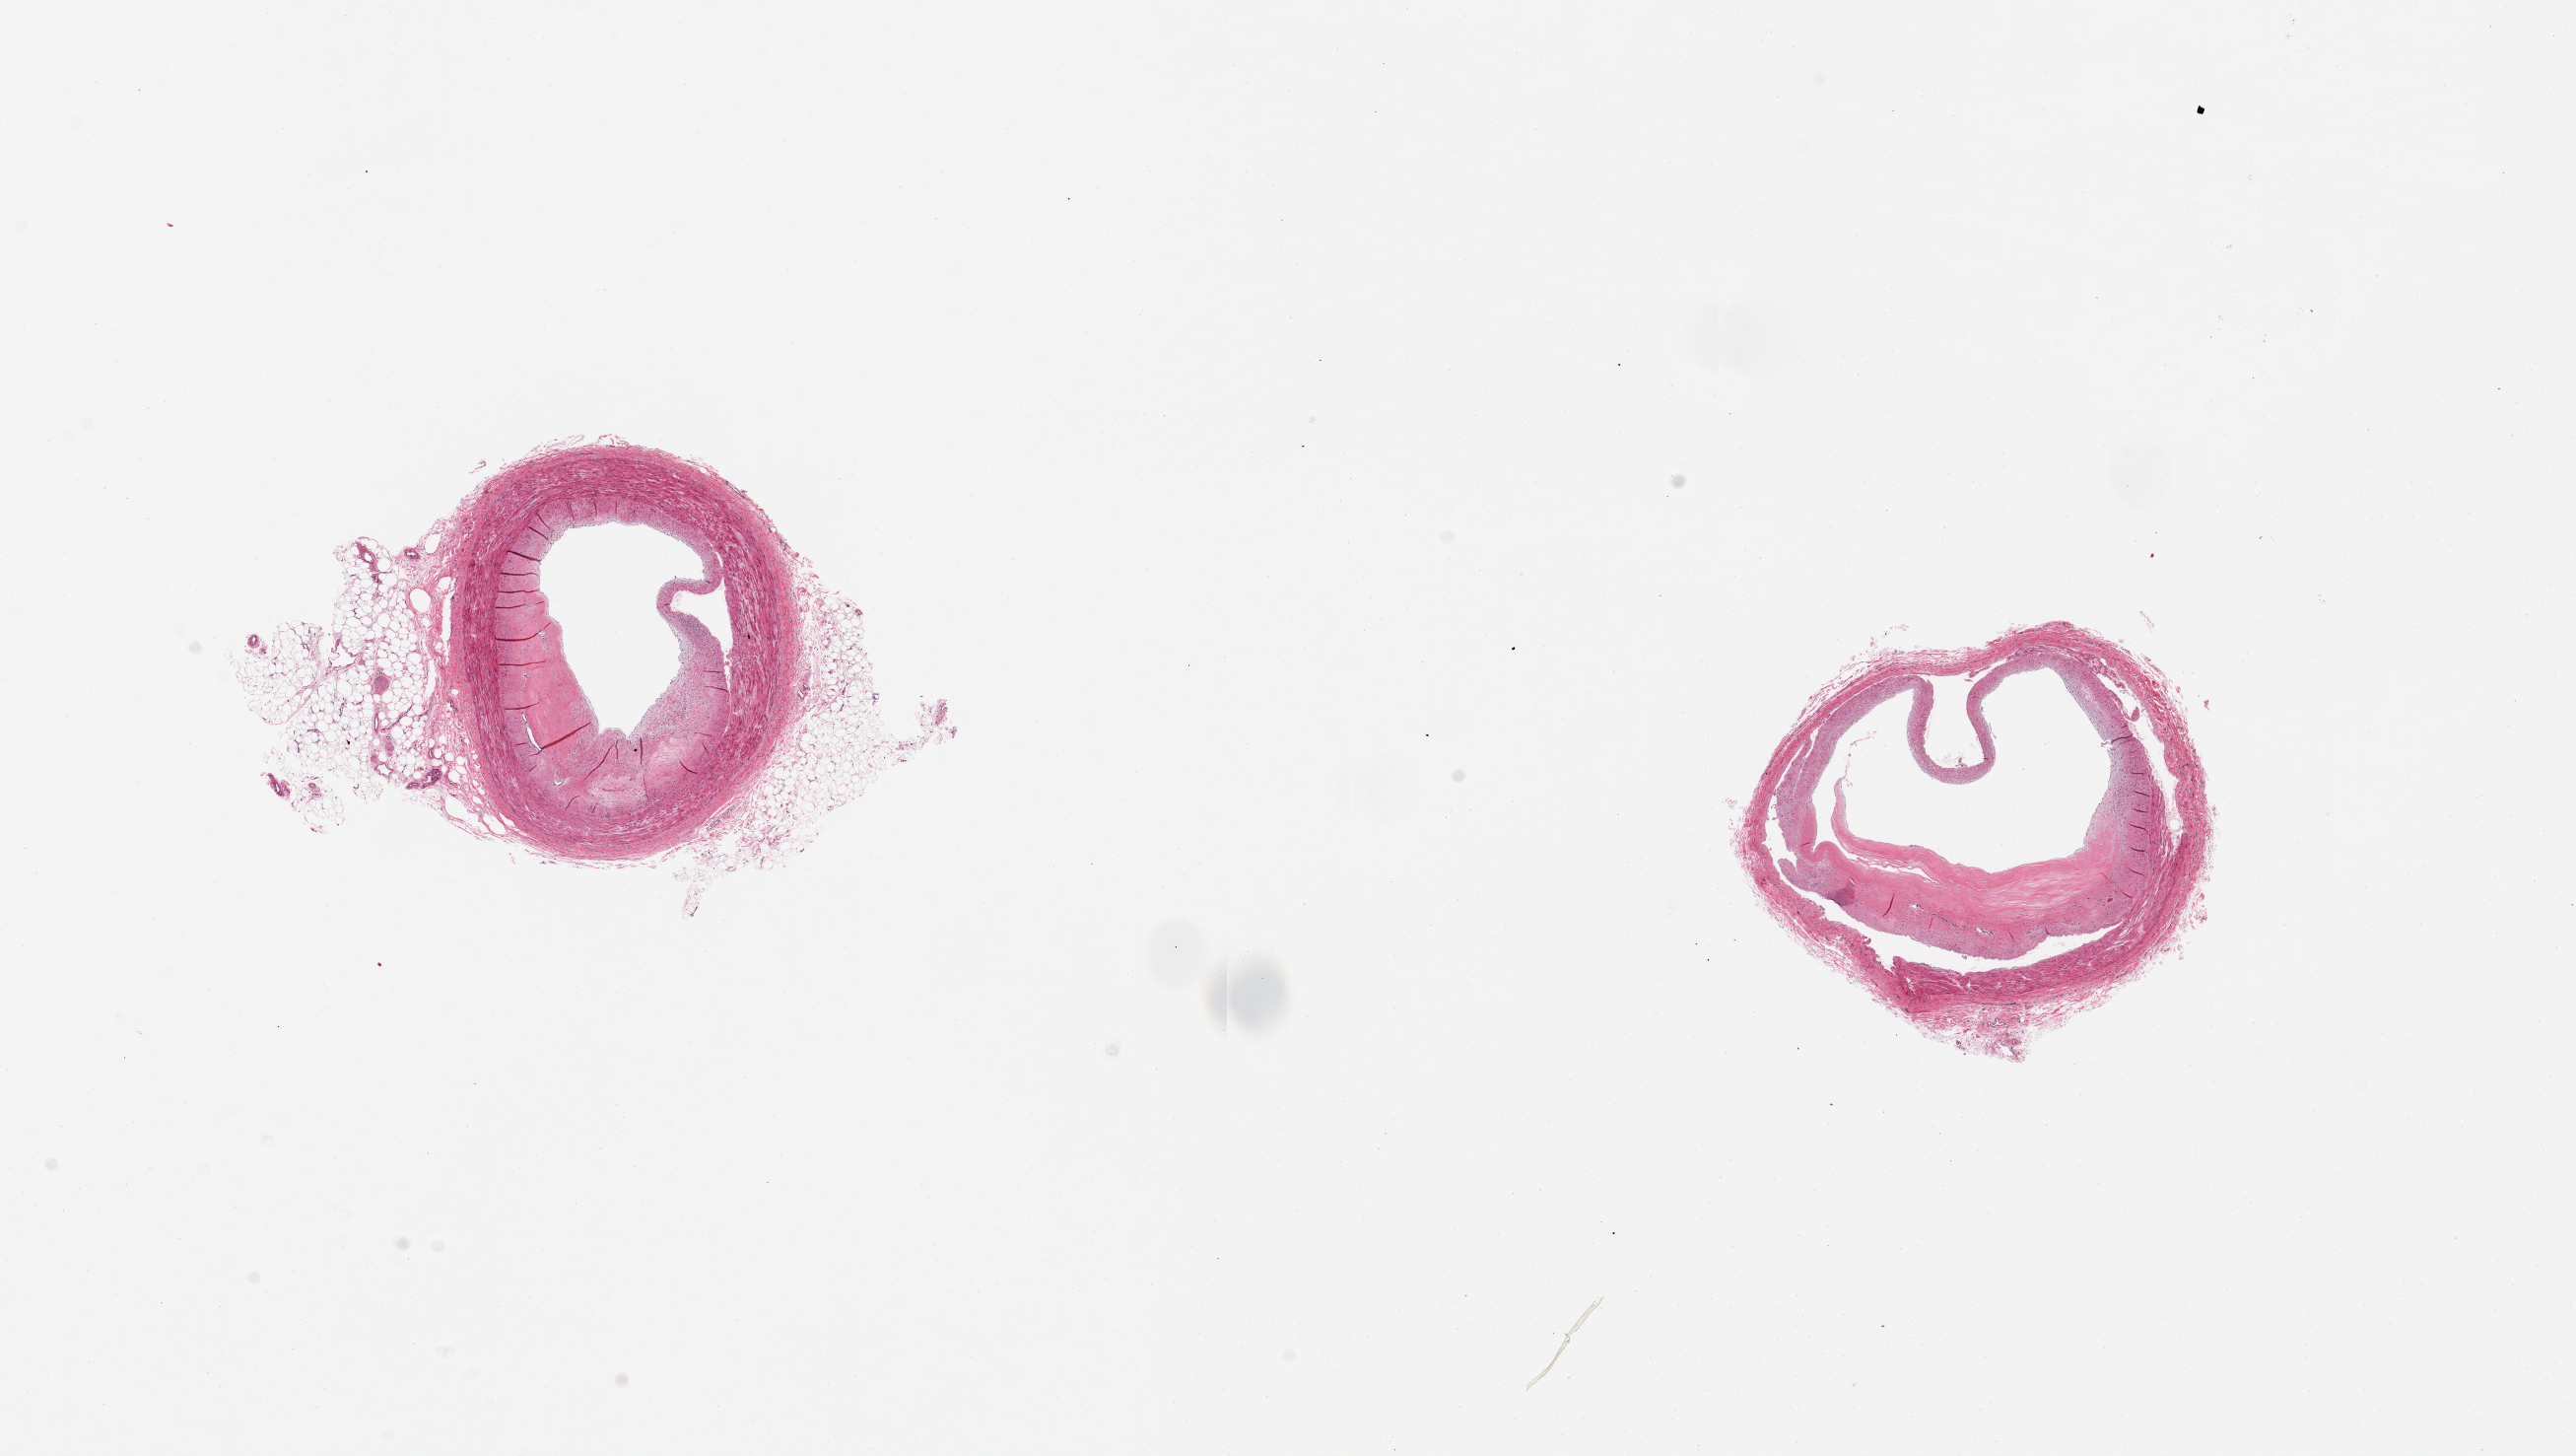
Haematoxylin and eosin whole-slide image, brightfield, shown as a low-resolution overview of the whole scanned area (about 20.7 x 11.7 mm). PAXgene-fixed, paraffin-embedded tissue. Section of coronary artery (target tissue). Tissue donor sample. Female donor.
Pathologist's review note for this sample: 2 pieces, 6x4 & 4x3.5mm. 1 well trimmed, 1 with up to 1.5 mm external adipose. Moderate eccentric plaque but wide lumen.